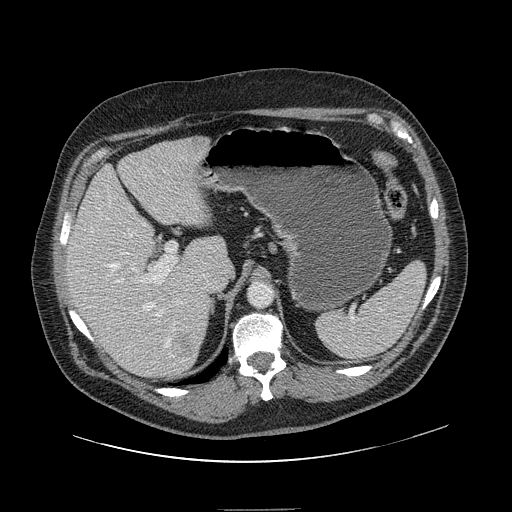
Contrast-enhanced abdominal CT, one axial slice; slice 96 of 154 in the series (ordered by position); 120 kVp; intravenous contrast given; soft-tissue window (W 400 / L 40 HU); 512 × 512 image matrix. Male patient, age 61 years. Case-level facts recorded for this patient, not image findings: diagnosis: colorectal cancer liver metastases, imaged before liver resection; multiple liver metastases: yes; largest metastasis: 2.6 cm; chemotherapy before resection: no.
Outlined on this slice (outlined manually by an expert reader):
- hepatic veins: bounding box [x1, y1, x2, y2] px = [91, 212, 178, 348]
- liver: [68, 138, 225, 379]
- planned liver remnant (the part of the liver to remain after resection): [68, 146, 225, 363]
- portal vein (with intrahepatic branches): [110, 200, 180, 304]
- liver metastasis: [189, 141, 206, 155]
- liver metastasis: [181, 344, 191, 352]